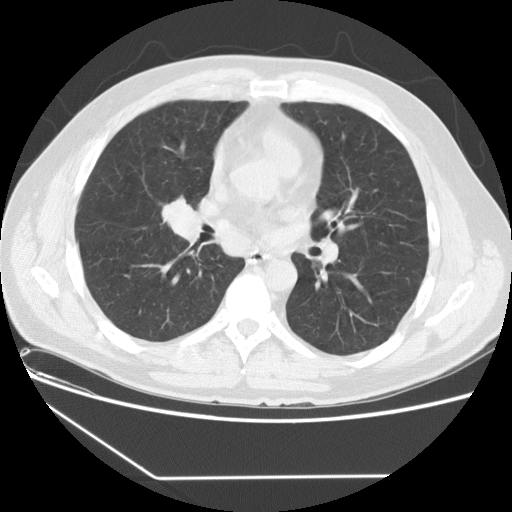
Low-dose screening chest CT, one axial slice; position 78 of 154 along the scan axis; lung window (W 1500 / L -600 HU); 2.5 mm slice thickness; 512 × 512 image matrix, field of view 370 × 370 mm.
Annotated regions visible in this slice (manually delineated by an expert):
- lesion 1 (tumor, middle lobe of right lung): bounding box (x1, y1, x2, y2) in pixels: (163, 202, 201, 239)